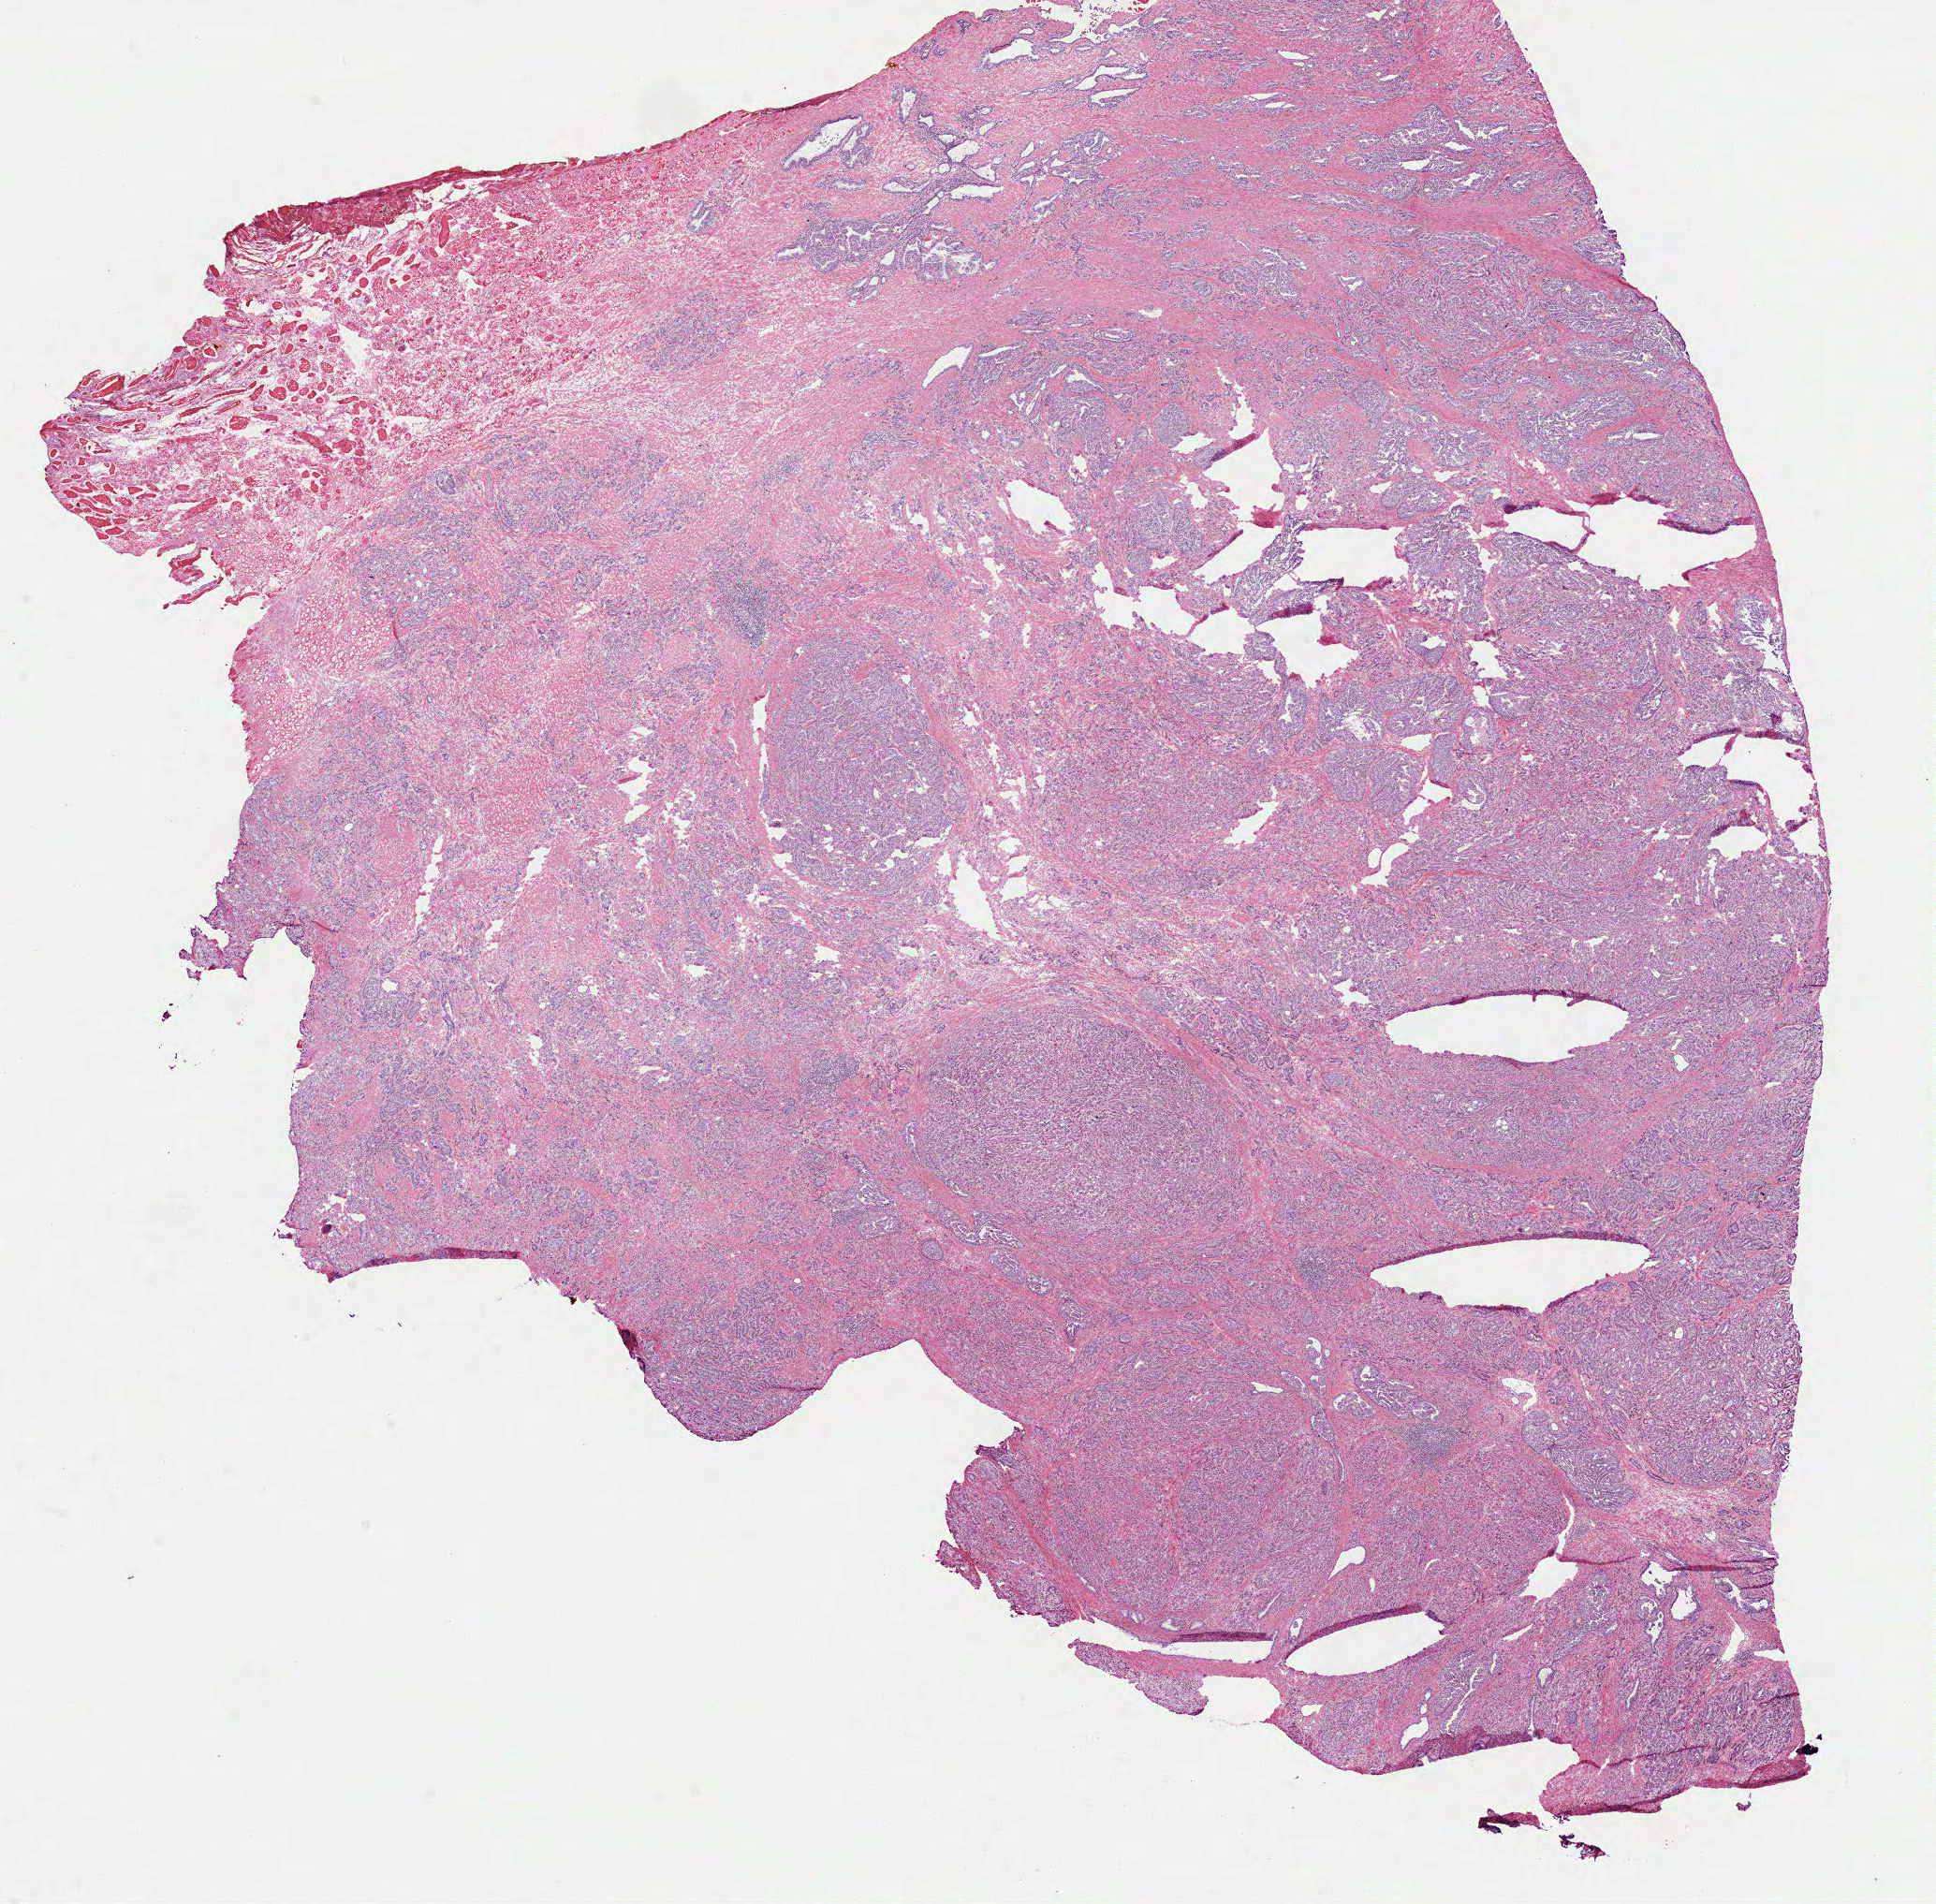
Digitized H&E-stained tissue section (whole slide) — shown as a low-resolution overview of the whole scanned area (about 16.7 x 16.4 mm, acquisition: 40x scan); frozen section; primary tumour sample from the prostate. Male patient; age at initial diagnosis 53 years. Gleason score: 7 (3+4). Composition of this section per pathologist review: tumour cells 90%, tumour nuclei 95%, normal cells 2%, stromal cells 8%, necrosis 0%. Inflammatory infiltration, as recorded: lymphocyte infiltration 2%, monocyte infiltration 0%, neutrophil infiltration 0%.
* lymph nodes positive (case pathology): 0 of 6 examined
* pathologic diagnosis: Acinar cell carcinoma (prostate gland)